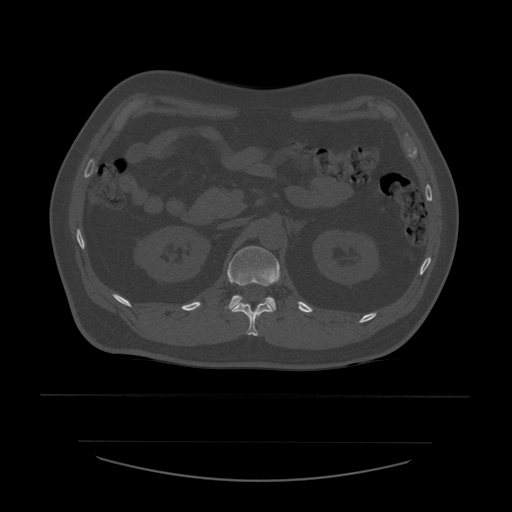
CT including the spine, one axial slice. Slice 238 of 532 in the series (ordered by position). Reconstruction kernel STANDARD. Bone window (W 1800 / L 400 HU). 512 × 512 image matrix. Patient age 44 years. From the clinical record (not read from this slice): primary cancer: soft tissue sarcoma.
Outlined on this slice (semi-automatically segmented with operator editing):
- L1 vertebra: bounding box [x1, y1, x2, y2] px = [228, 246, 281, 313]
- T12 vertebra: [232, 301, 273, 336]